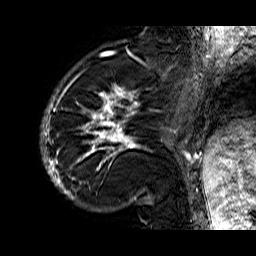
Breast MRI (dynamic contrast-enhanced), one sagittal slice; position 14 of 60 along the scan axis; dynamic contrast-enhanced series, time point 2 of 6 at this slice position (early post-contrast); 1.5 T; TE 6.3 ms, TR 32.9 ms; 4 mm slice thickness; 256 × 256 image matrix. Female patient. Case-level facts recorded for this patient, not image findings: setting: breast cancer imaged before/during neoadjuvant chemotherapy; receptor status: HR-positive, HER2-negative.
Outlined on this slice (semi-automatically segmented with operator editing):
- analysis volume of interest (the breast-tissue region the enhancement analysis was run in; not a lesion): bounding box <40,74,176,210> (left, top, right, bottom; pixels)
- tumour enhancement mask (voxels above the 100 % enhancement threshold inside the analysis volume of interest): <40,74,176,203>